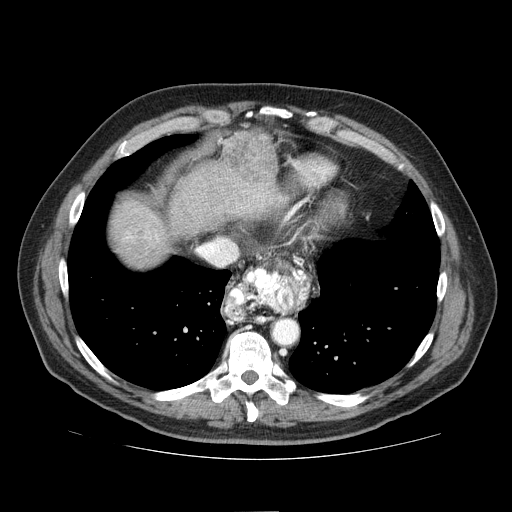
Contrast-enhanced abdominal CT (liver protocol), one axial slice. Position 67 of 81 along the scan axis. 100 kVp. One of 2 acquisitions stored at this slice position. Soft-tissue window (W 400 / L 40 HU). 2.5 mm slice thickness. 512 × 512 image matrix, field of view 400 × 400 mm. Case-level facts recorded for this patient, not image findings: diagnosis: hepatocellular carcinoma (patient treated with transarterial chemoembolisation; whether this scan precedes or follows treatment is not stated here); TNM stage (as recorded): Stage-IIIA; Child-Pugh class: A.
Annotated regions visible in this slice (semi-automatic segmentation, software-assisted and operator-edited):
- liver parenchyma outside the tumour (the mass and vessels are separate outlines, so this box may not span the whole liver): bounding box [x1, y1, x2, y2] px = [111, 162, 288, 268]
- mass: [221, 128, 278, 185]
- liver vessels: [125, 191, 264, 241]